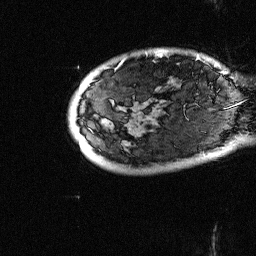
Breast MRI (dynamic contrast-enhanced), one sagittal slice; position 7 of 64 along the scan axis; dynamic contrast-enhanced study with each time point stored as its own series, time point 2 of 3 at this slice position (early post-contrast, ordered by acquisition time); 1.5 T; TE 4.5 ms, TR 11 ms; 2.5 mm slice thickness; 256 × 256 image matrix, field of view 200 × 200 mm. Patient: female, 38 years. Case-level facts recorded for this patient, not image findings: setting: breast cancer imaged before/during neoadjuvant chemotherapy; receptor status: HR-positive, HER2-negative.
Structures marked on this image (semi-automatic segmentation, software-assisted and operator-edited):
- analysis volume of interest (the breast-tissue region the enhancement analysis was run in; not a lesion): box from (x=88, y=25) to (x=252, y=126) px
- tumour enhancement mask (voxels above the 90 % enhancement threshold inside the analysis volume of interest): (x=156, y=54)–(x=161, y=57)